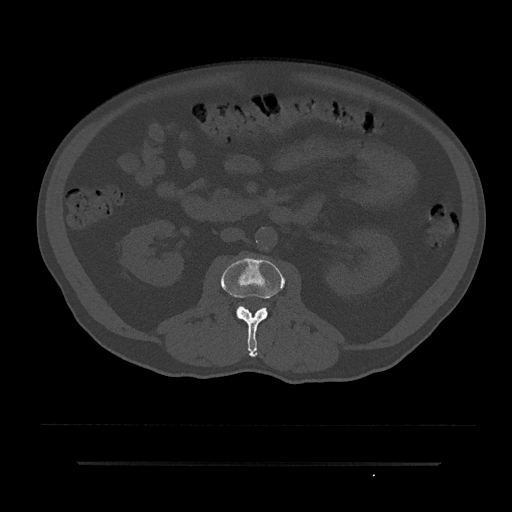
CT including the spine, one axial slice; position 55 of 797 along the scan axis; bone window (W 1800 / L 400 HU); 0.5 mm slice thickness; 512 × 512 image matrix, field of view 464 × 464 mm. Male patient, age 59 years. Case-level facts recorded for this patient, not image findings: primary cancer: bile ducts; vertebrae with lytic lesions (as recorded): T10.
Annotated regions visible in this slice (semi-automatically segmented with operator editing):
- L2 vertebra: bounding box <221,257,285,357> (left, top, right, bottom; pixels)